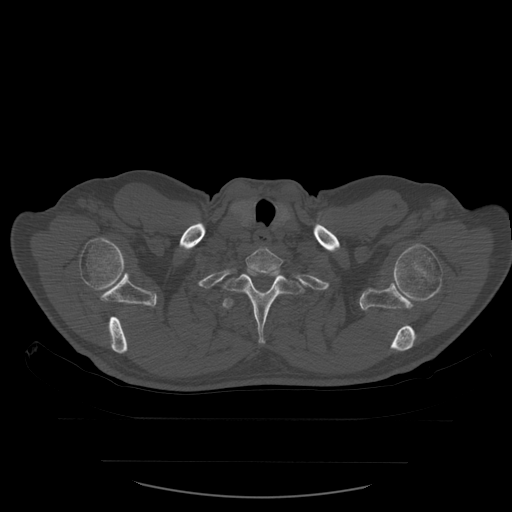
CT including the spine, one axial slice; position 477 of 590 along the scan axis; bone window (W 1800 / L 400 HU); 512 × 512 image matrix, field of view 479 × 479 mm. Patient age 71 years. Case-level facts recorded for this patient, not image findings: primary cancer: lung.
Structures marked on this image (semi-automatically segmented with operator editing):
- T1 vertebra: bounding box <246,247,283,275> (left, top, right, bottom; pixels)
- T2 vertebra: <223,269,309,344>
- T3 vertebra: <222,298,237,311>